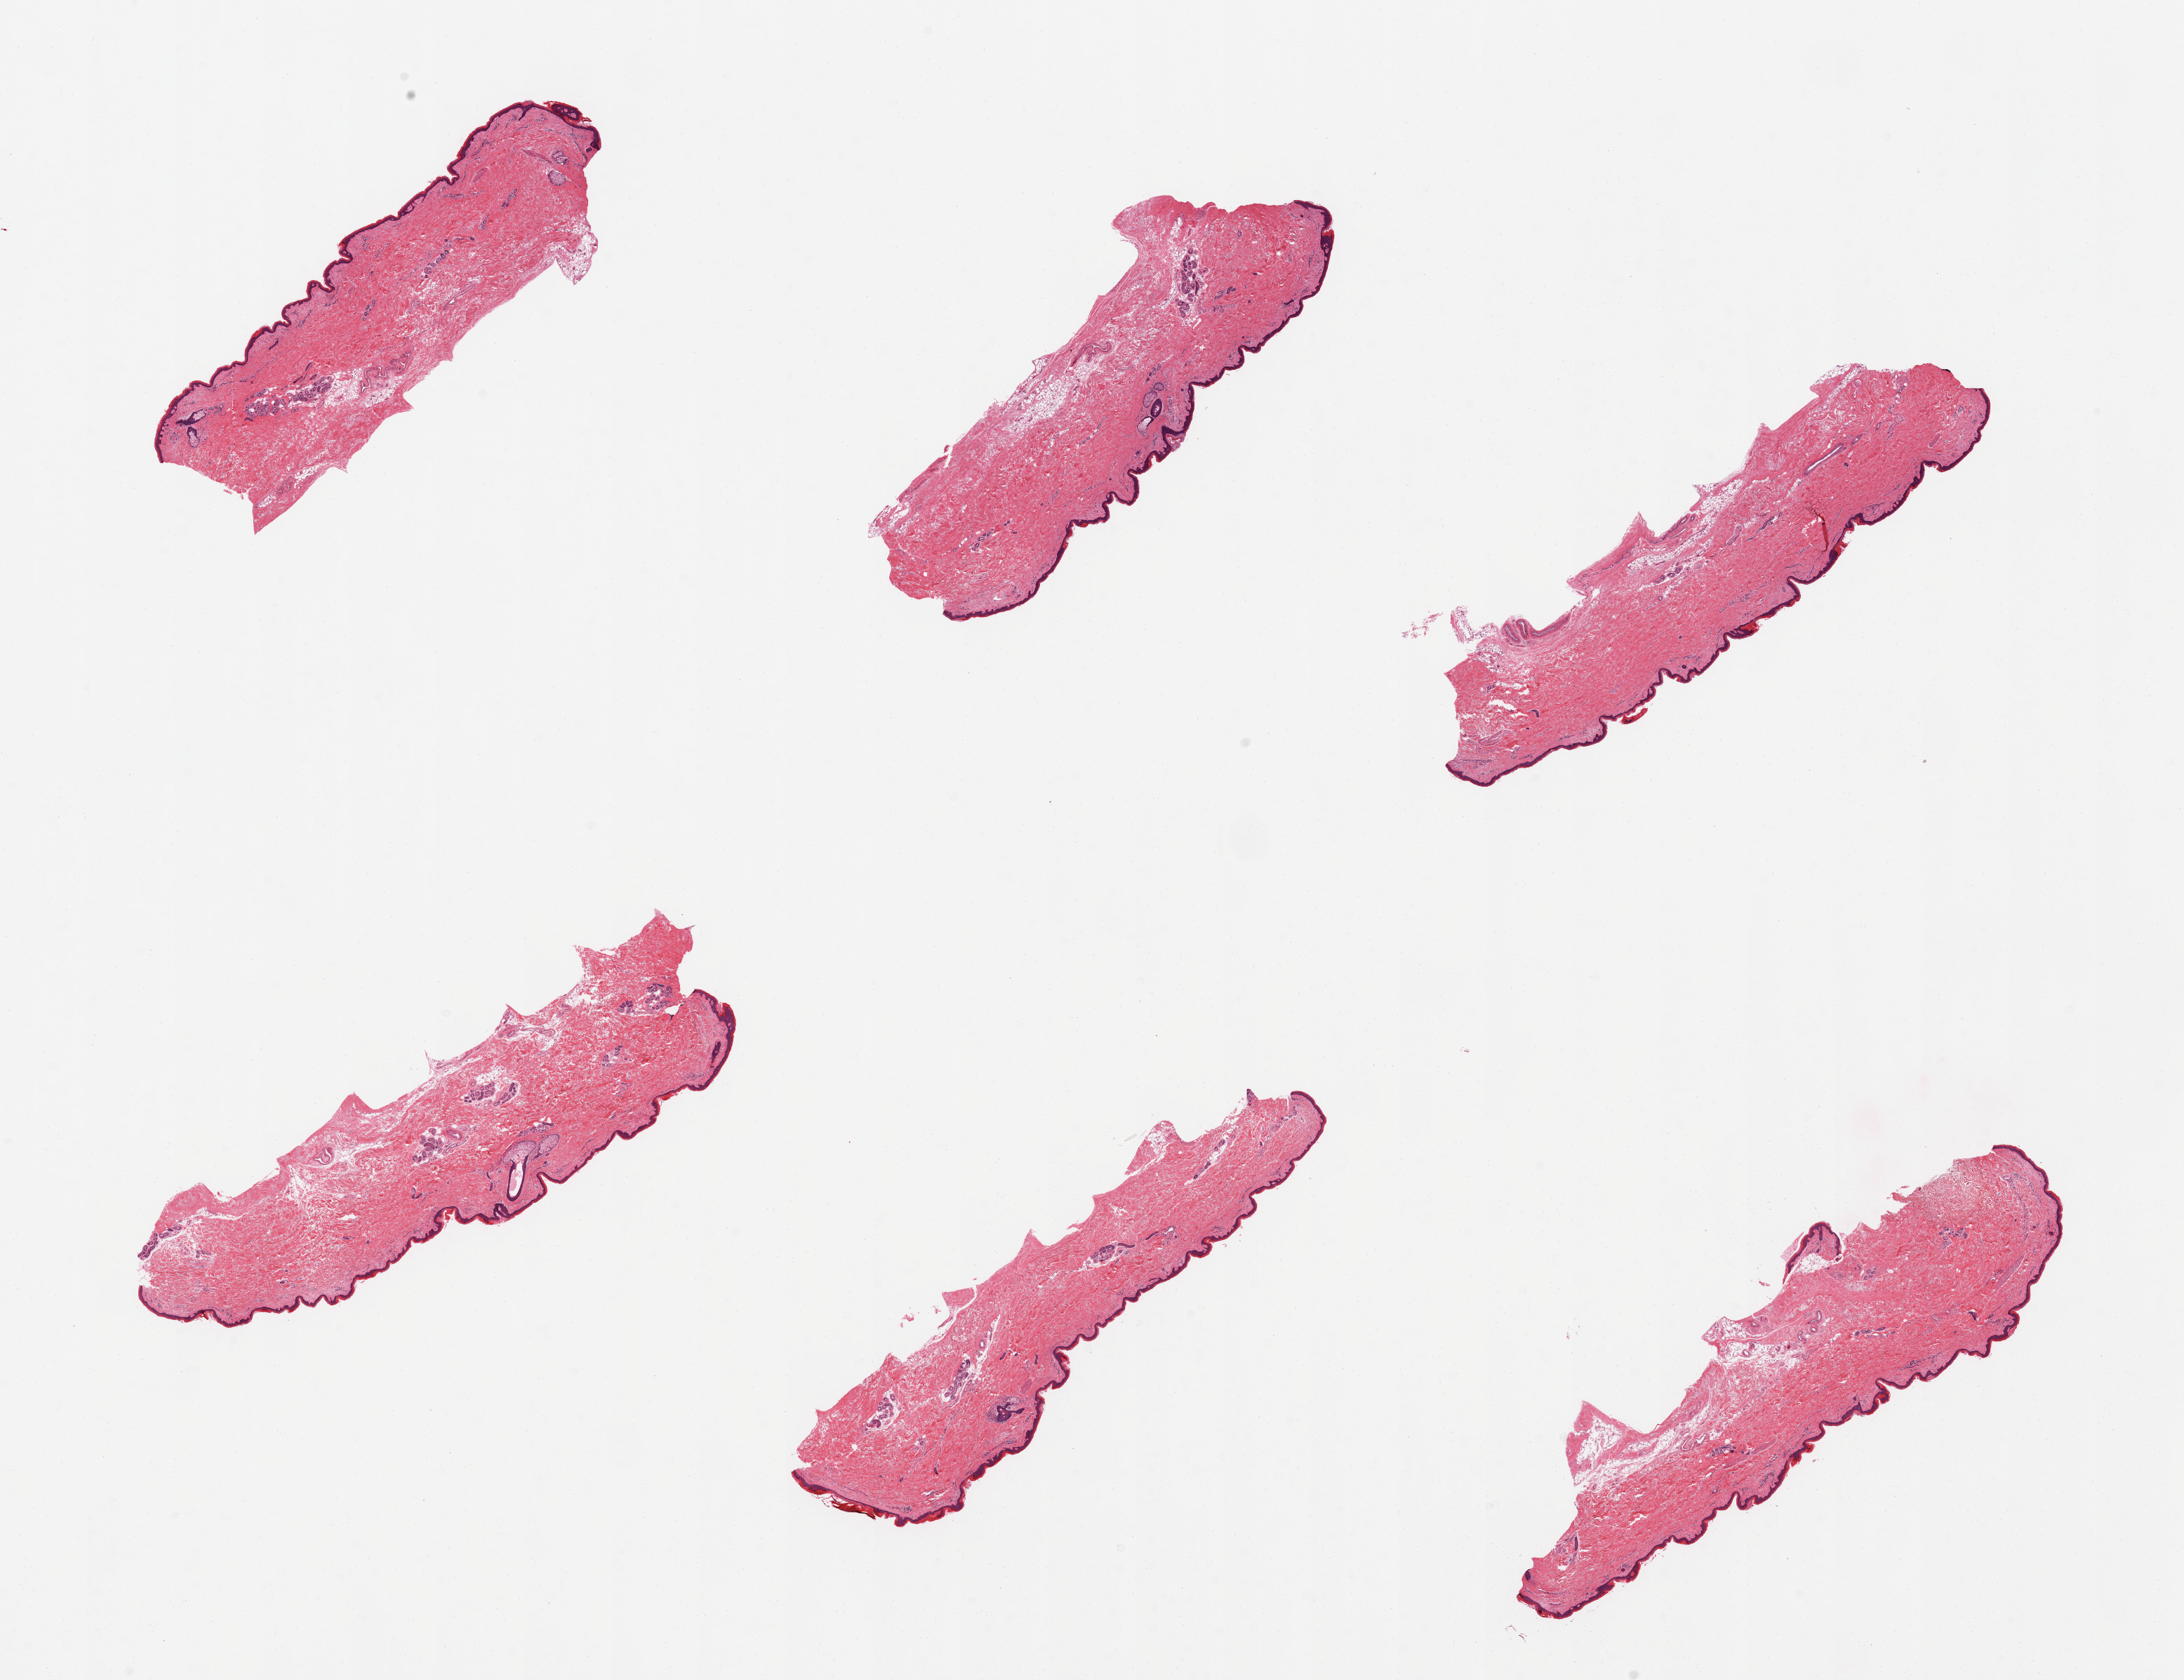
Digitized haematoxylin and eosin-stained section, brightfield, a low-resolution overview of the entire scanned area, about 24.6 x 18.9 mm. PAXgene-fixed, paraffin-embedded tissue. Sampled site (target tissue): skin of lower leg. Tissue donor sample. Male donor.
Review note (as recorded): 6 pieces, minimal dermal fat; squamous epithelium is ~30 microns.